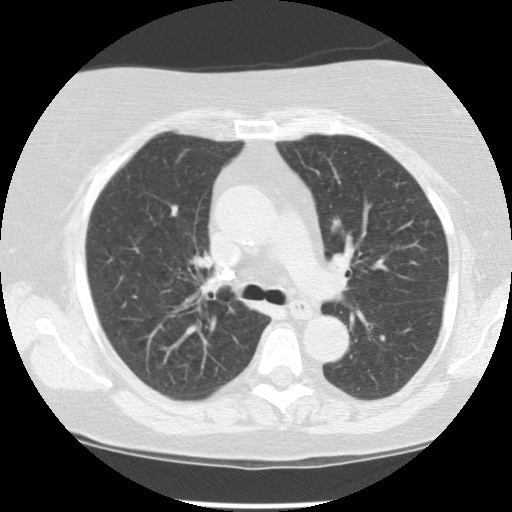
Axial slice from a low-dose chest CT screening exam, first (baseline) screen, lung window (W 1500 / L -600 HU), standard (soft-tissue) reconstruction kernel (STANDARD), slice 36 of 108 in the series. Female participant, aged 67 years at enrolment. Former smoker at enrolment.
• Lesion marked by an expert reader, bounding box [x1, y1, x2, y2] px = [309, 207, 365, 257].
• Reader record for this screening exam (exam-level; its link to the box is not recorded): non-calcified nodule or mass ≥4 mm, left upper lobe, 13 × 10 mm, poorly defined margins, soft tissue attenuation.
• Participant outcome: lung cancer diagnosed 399 days after this screen (after the second annual screen) — adenocarcinoma, NOS, left upper lobe, moderately differentiated (G2), stage IIA (AJCC 6th edition), 23 mm at pathology.